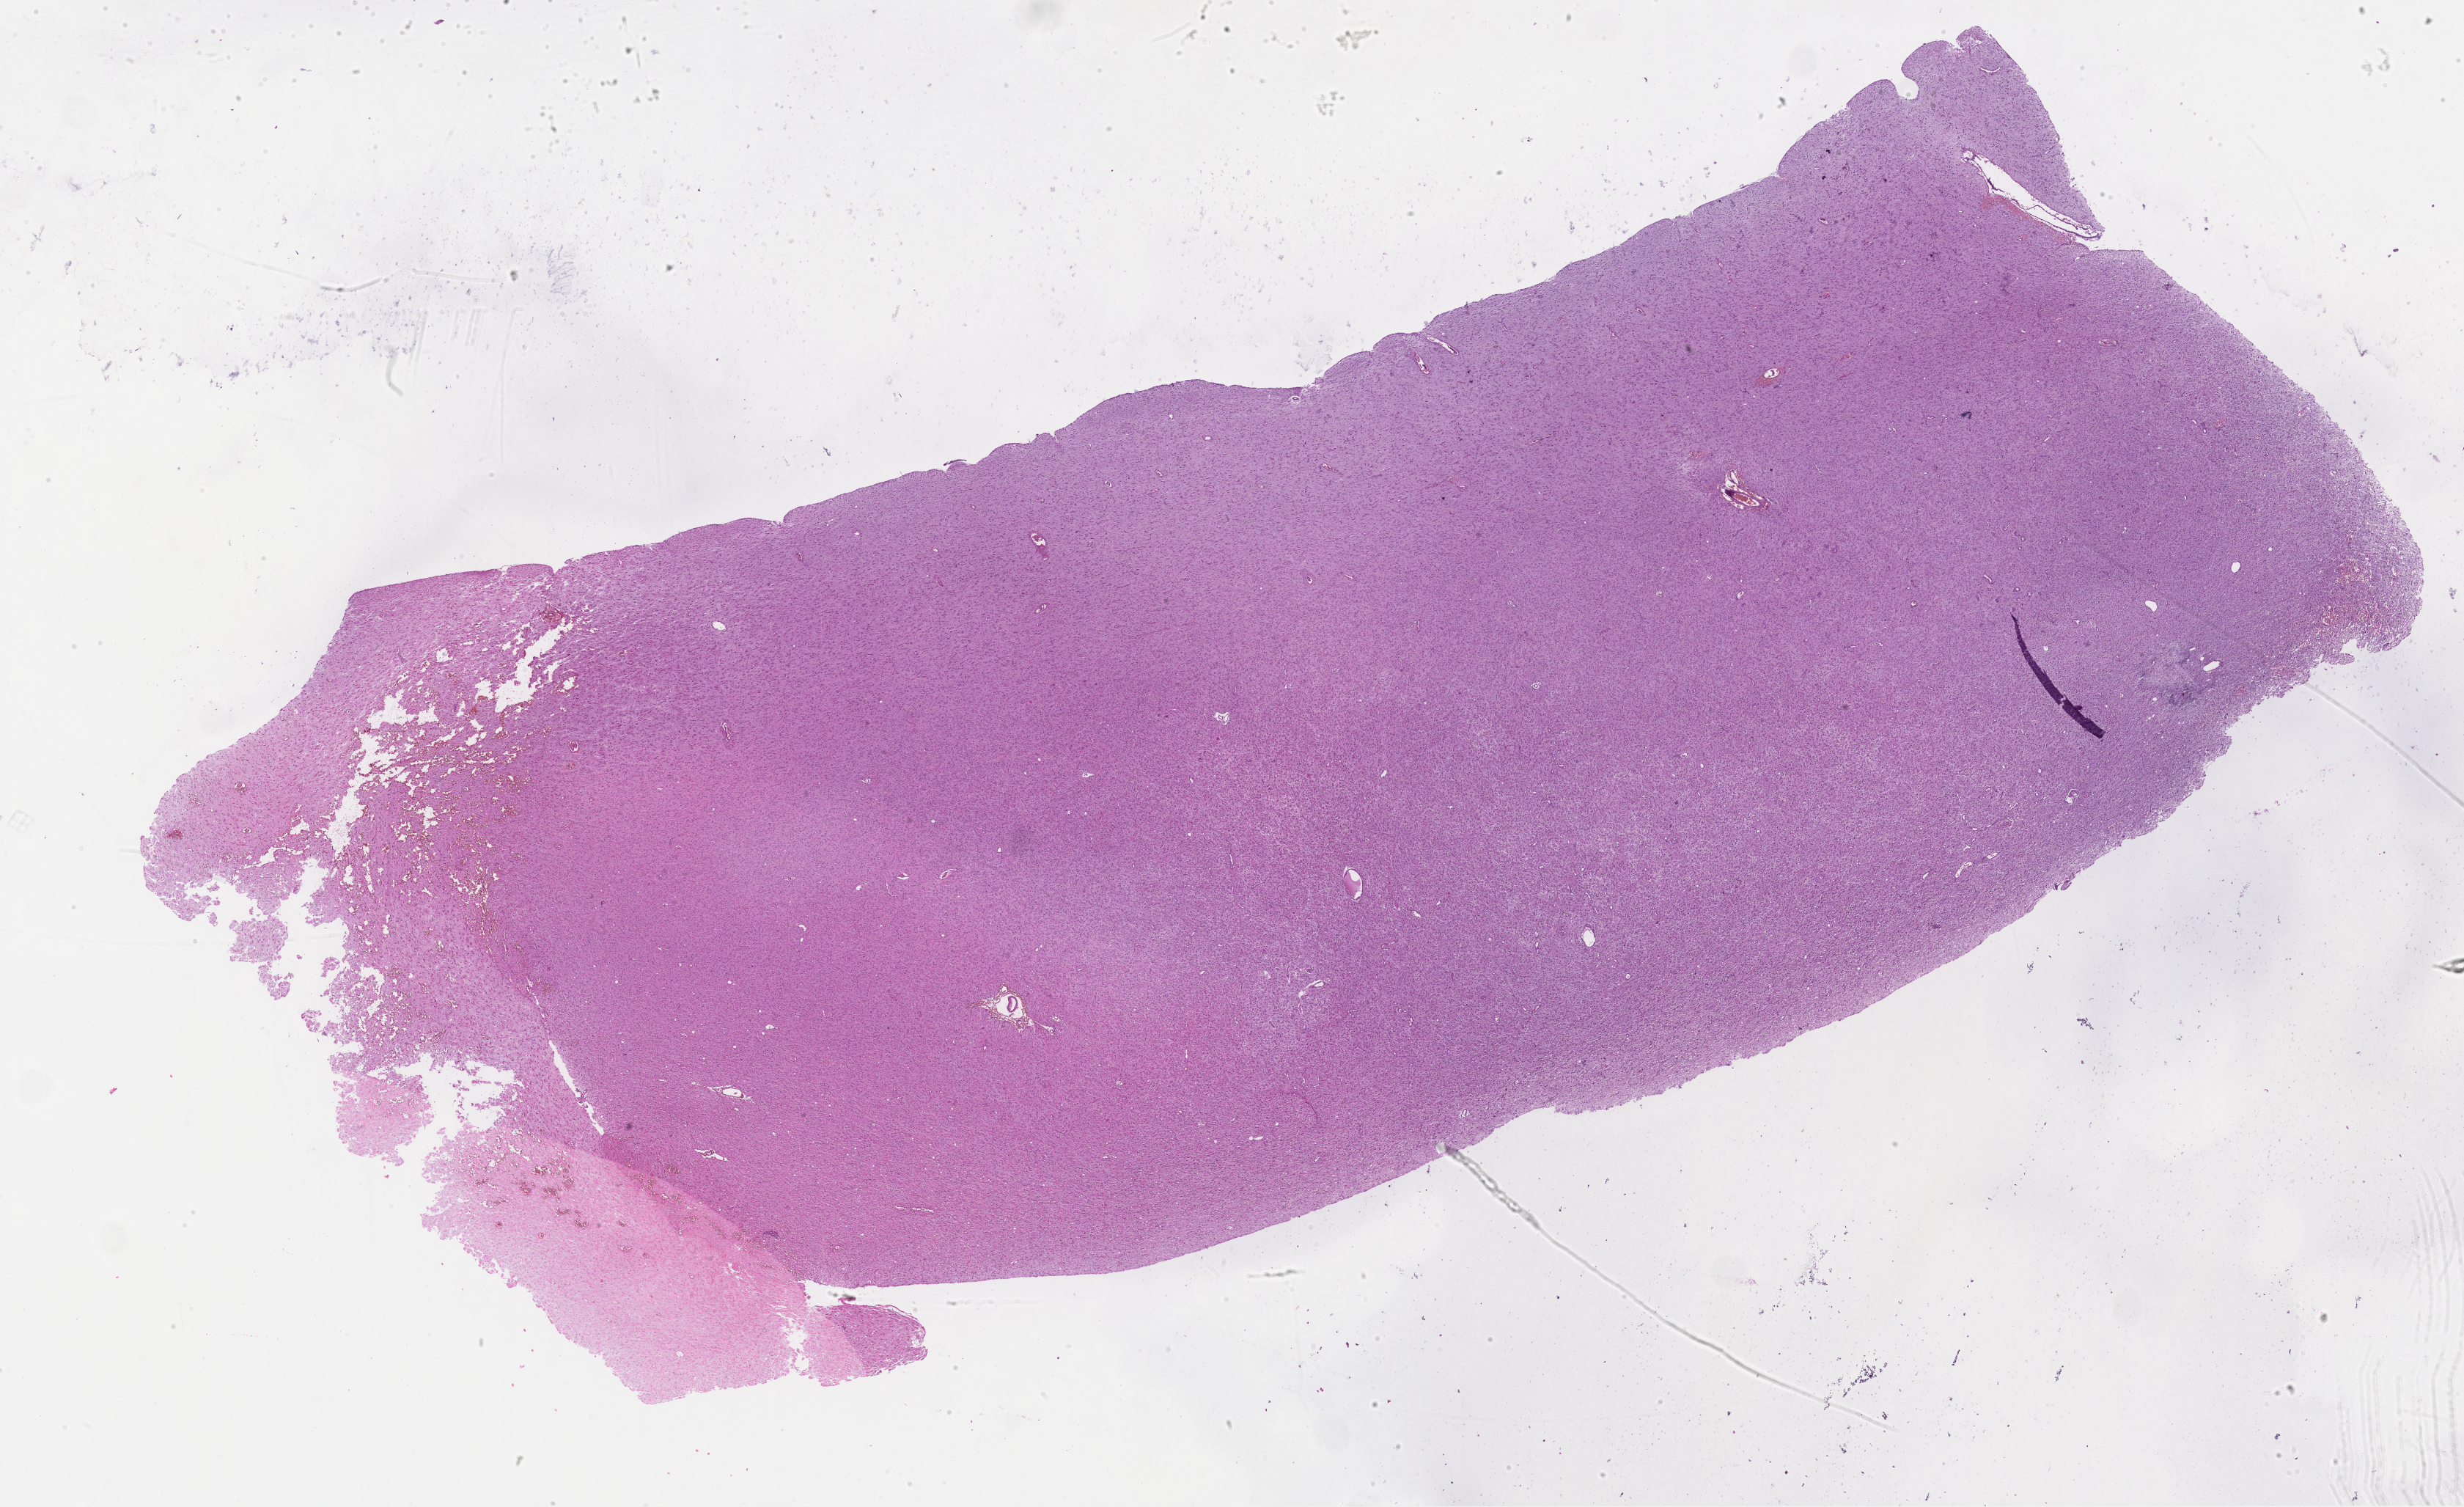
Whole-slide histology image, H&E-stained — shown as a low-resolution overview of the whole scanned area (about 27.2 x 16.7 mm, slide scanned at 40x); FFPE section; brain, primary tumour sample. Male patient; age at initial diagnosis 50 years.
Pathologic diagnosis: Glioblastoma.